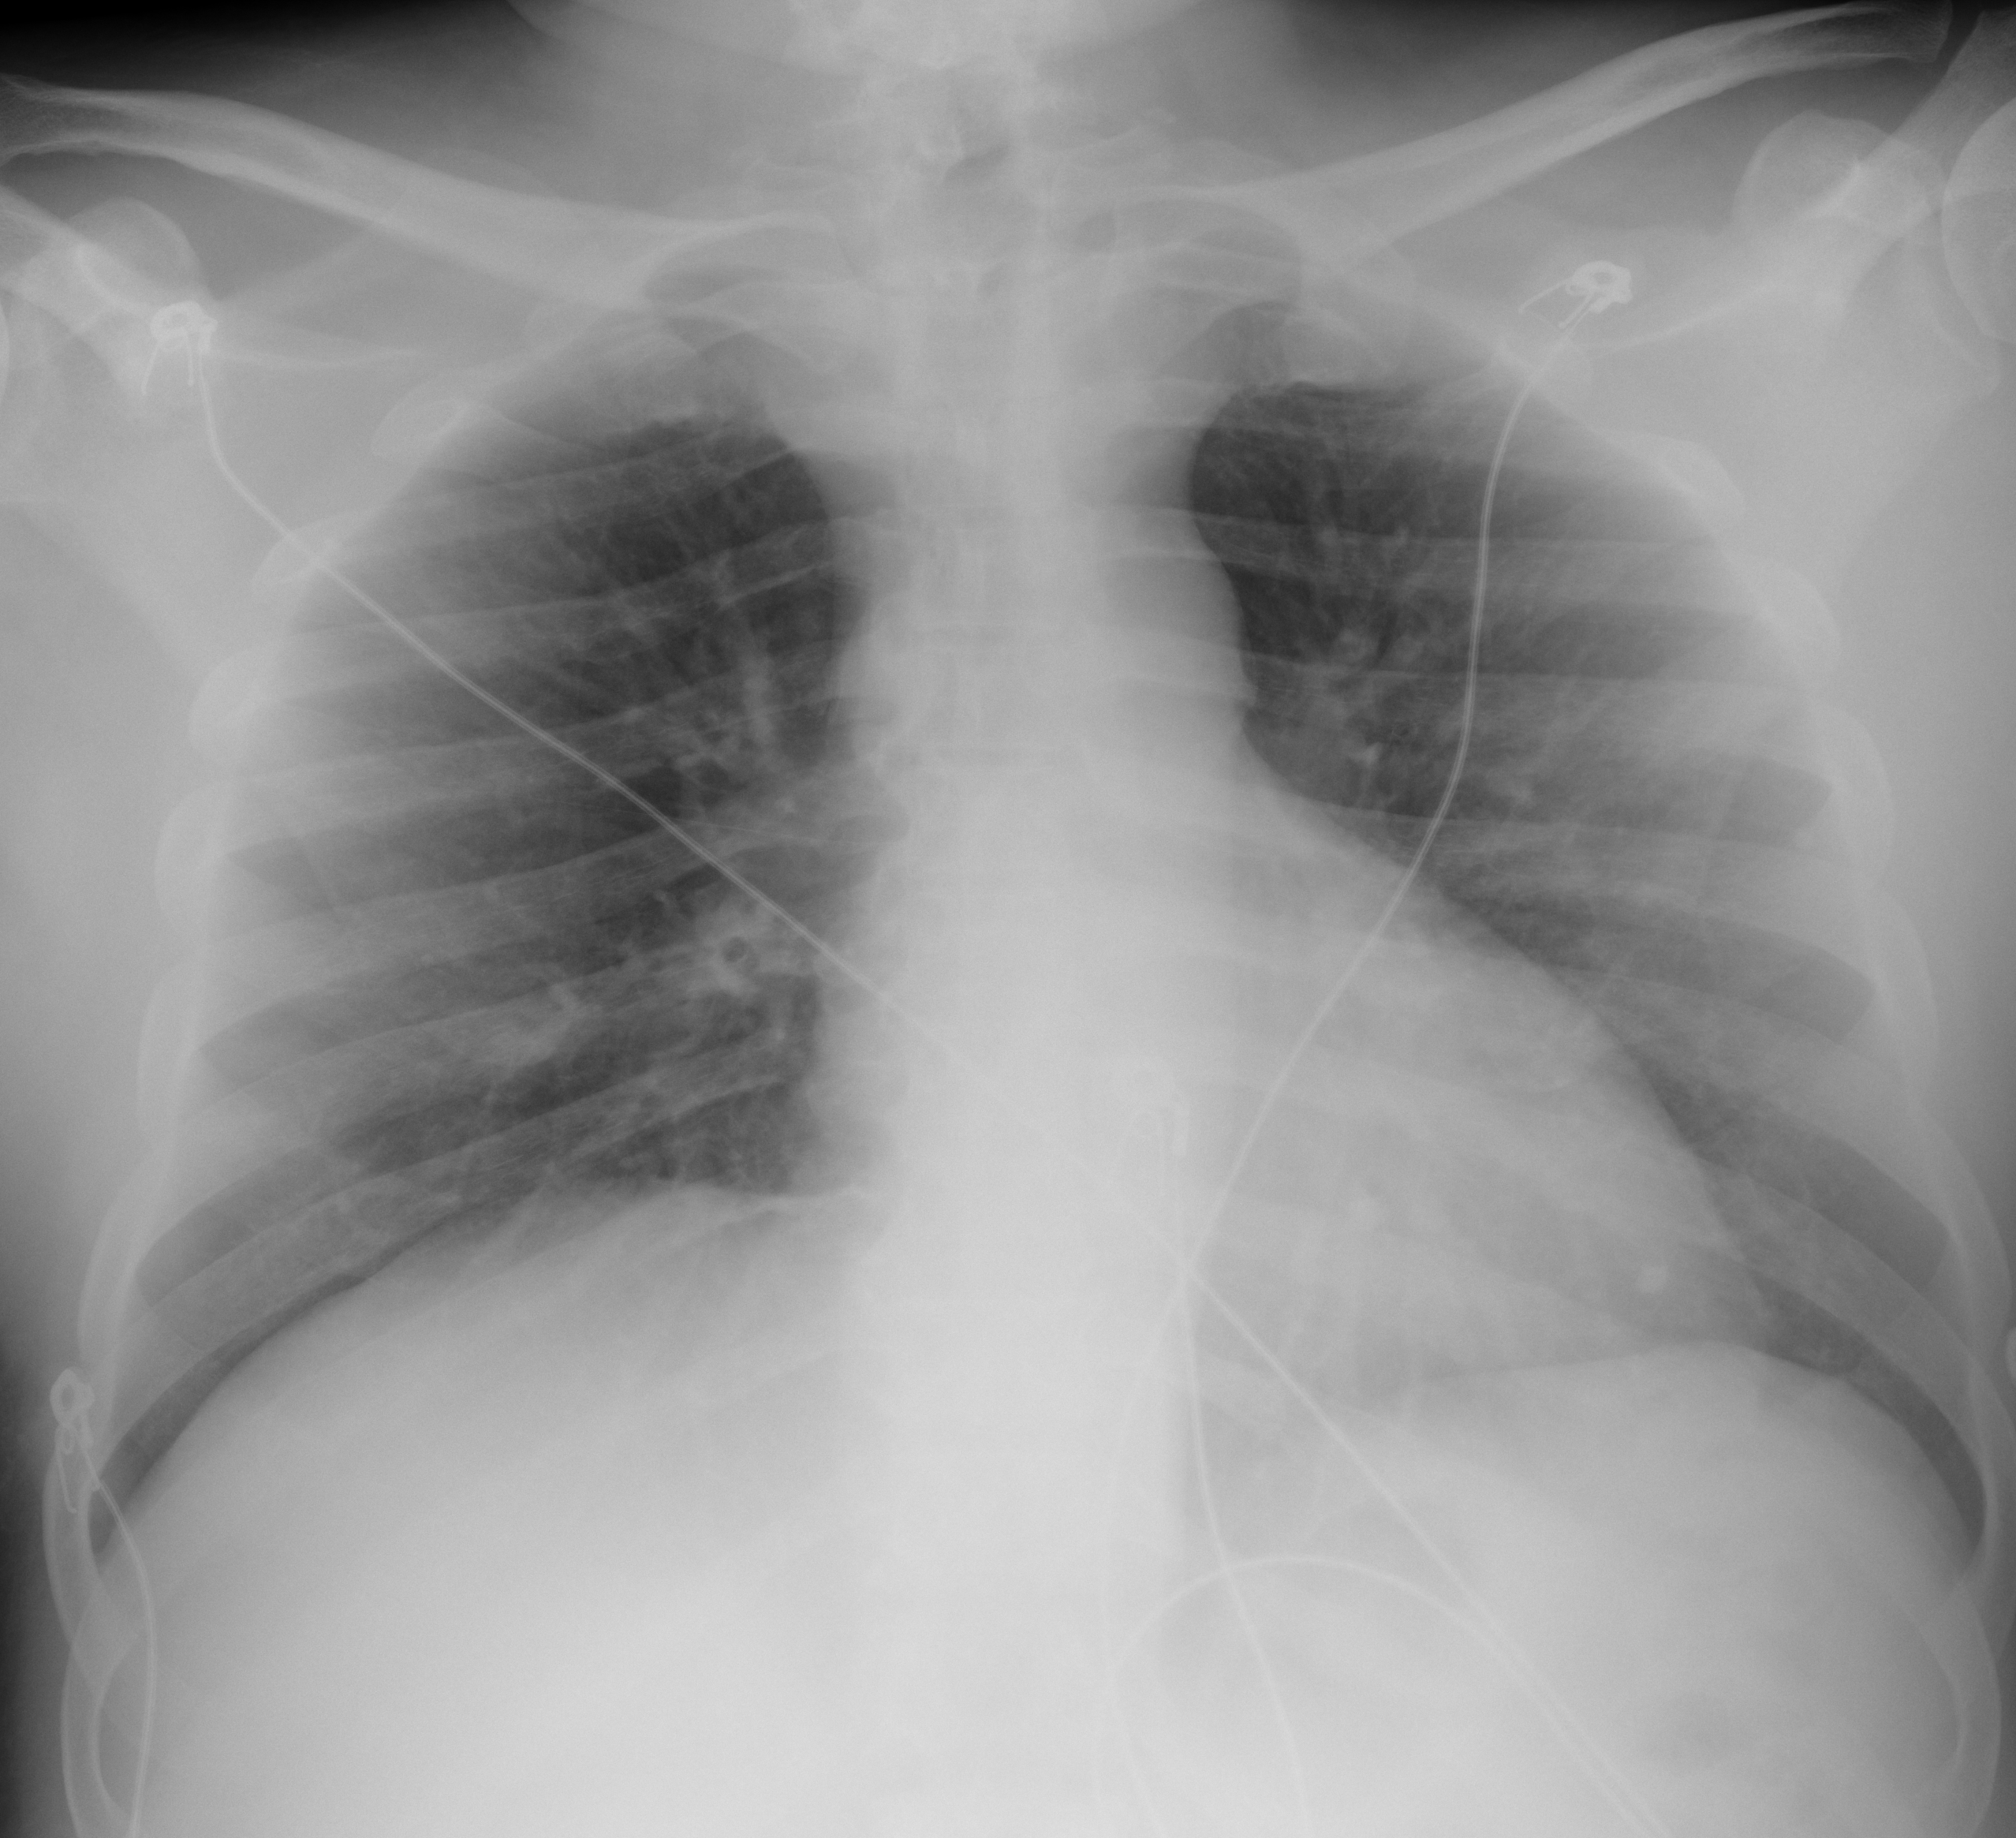
Portable chest radiograph, AP projection. Male patient, age 55 years; imaged 0 days after the COVID-19 diagnosis.
Radiologist's key findings for this exam: Lungs are clear with no nodule, airspace disease or pleural effusion.